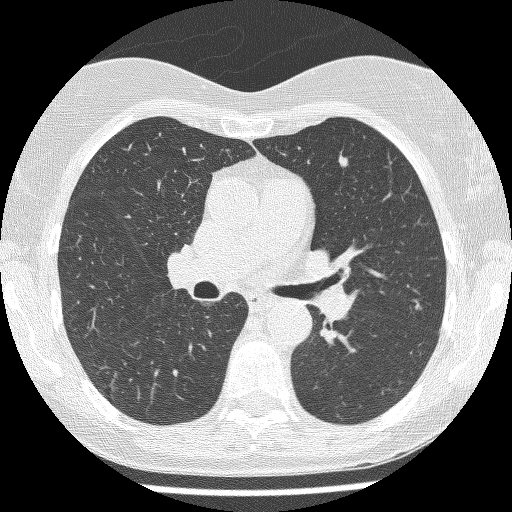
Chest CT (low-dose screening protocol), one axial image; baseline screening round; lung window (W 1500 / L -600 HU); 1.25 mm slice thickness; lung (sharp) reconstruction kernel (BONE); 120 kVp; slice 148 of 237 in the series; 512 × 512 image matrix, field of view 280 × 280 mm. Female, age 60 years at enrolment. Current smoker at enrolment.
2 expert-annotated lung lesions on this slice (largest first), bounding box [x1, y1, x2, y2] px = [329, 150, 359, 174]; [404, 296, 431, 321]. The exam's reader record, not a measurement of the box and not confirmed to be the same lesion: non-calcified nodule or mass ≥4 mm, lingula, 5 × 4 mm, smooth margins, soft tissue attenuation. Official screen result: positive, change unspecified: nodule(s) >= 4 mm or enlarging nodule(s), mass(es), or other non-specific abnormalities suspicious for lung cancer. Participant outcome: lung cancer diagnosed 790 days after this screen (after the third annual screen) — adenocarcinoma, NOS, left upper lobe, moderately differentiated (G2), stage IA (AJCC 6th edition), 6 mm at pathology.